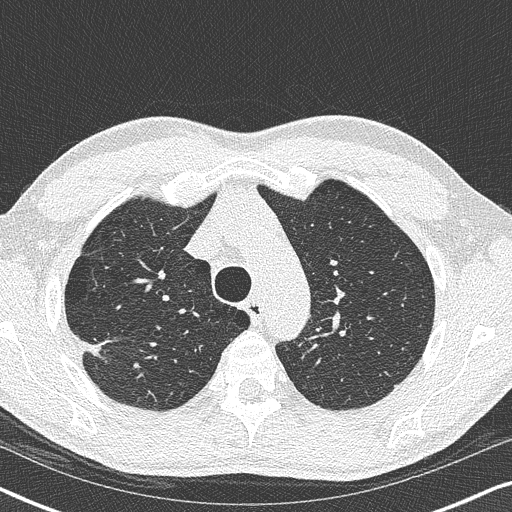
Low-dose screening chest CT, one axial slice. Position 283 of 356 along the scan axis. Reconstruction kernel B50f. 120 kVp. Lung window (W 1500 / L -600 HU). 1 mm slice thickness. 512 × 512 image matrix, field of view 330 × 330 mm.
Outlined on this slice (outlined manually by an expert reader):
- lesion 1 (tumor, upper lobe of right lung): bounding box <79,339,103,356> (left, top, right, bottom; pixels)